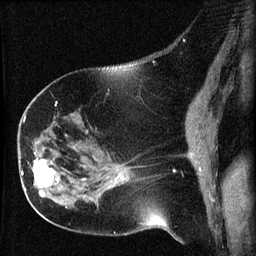
Breast MRI (dynamic contrast-enhanced), one sagittal slice. Position 27 of 60 along the scan axis. Dynamic contrast-enhanced series, image 2 of 3 at this slice position (ordered by acquisition). 1.5 T. TE 4.2 ms, TR 8.2 ms. 2 mm slice thickness. 256 × 256 image matrix, field of view 180 × 180 mm. Female patient, age 63 years.
Structures marked on this image (semi-automatic segmentation, software-assisted and operator-edited):
- analysis volume of interest (the breast-tissue region the enhancement analysis was run in; not a lesion): bounding box (x1, y1, x2, y2) in pixels: (22, 156, 64, 202)
- tumour enhancement mask (voxels above the 70 % enhancement threshold inside the analysis volume of interest): (22, 159, 54, 197)